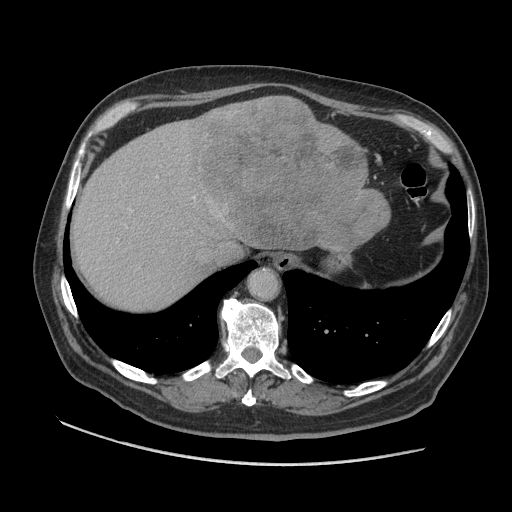
Contrast-enhanced abdominal CT (liver protocol), one axial slice; soft-tissue window (W 400 / L 40 HU); 2.5 mm slice thickness; 512 × 512 image matrix, field of view 420 × 420 mm. From the clinical record (not read from this slice): diagnosis: hepatocellular carcinoma (patient treated with transarterial chemoembolisation; whether this scan precedes or follows treatment is not stated here); TNM stage (as recorded): Stage-I; Child-Pugh class: A; tumour nodularity: uninodular.
Annotated regions visible in this slice (semi-automatically segmented with operator editing):
- abdominal aorta: bounding box [x1, y1, x2, y2] px = [251, 271, 276, 297]
- liver parenchyma outside the tumour (the mass and vessels are separate outlines, so this box may not span the whole liver): [72, 96, 366, 310]
- mass: [191, 96, 389, 255]
- liver vessels: [130, 176, 195, 211]